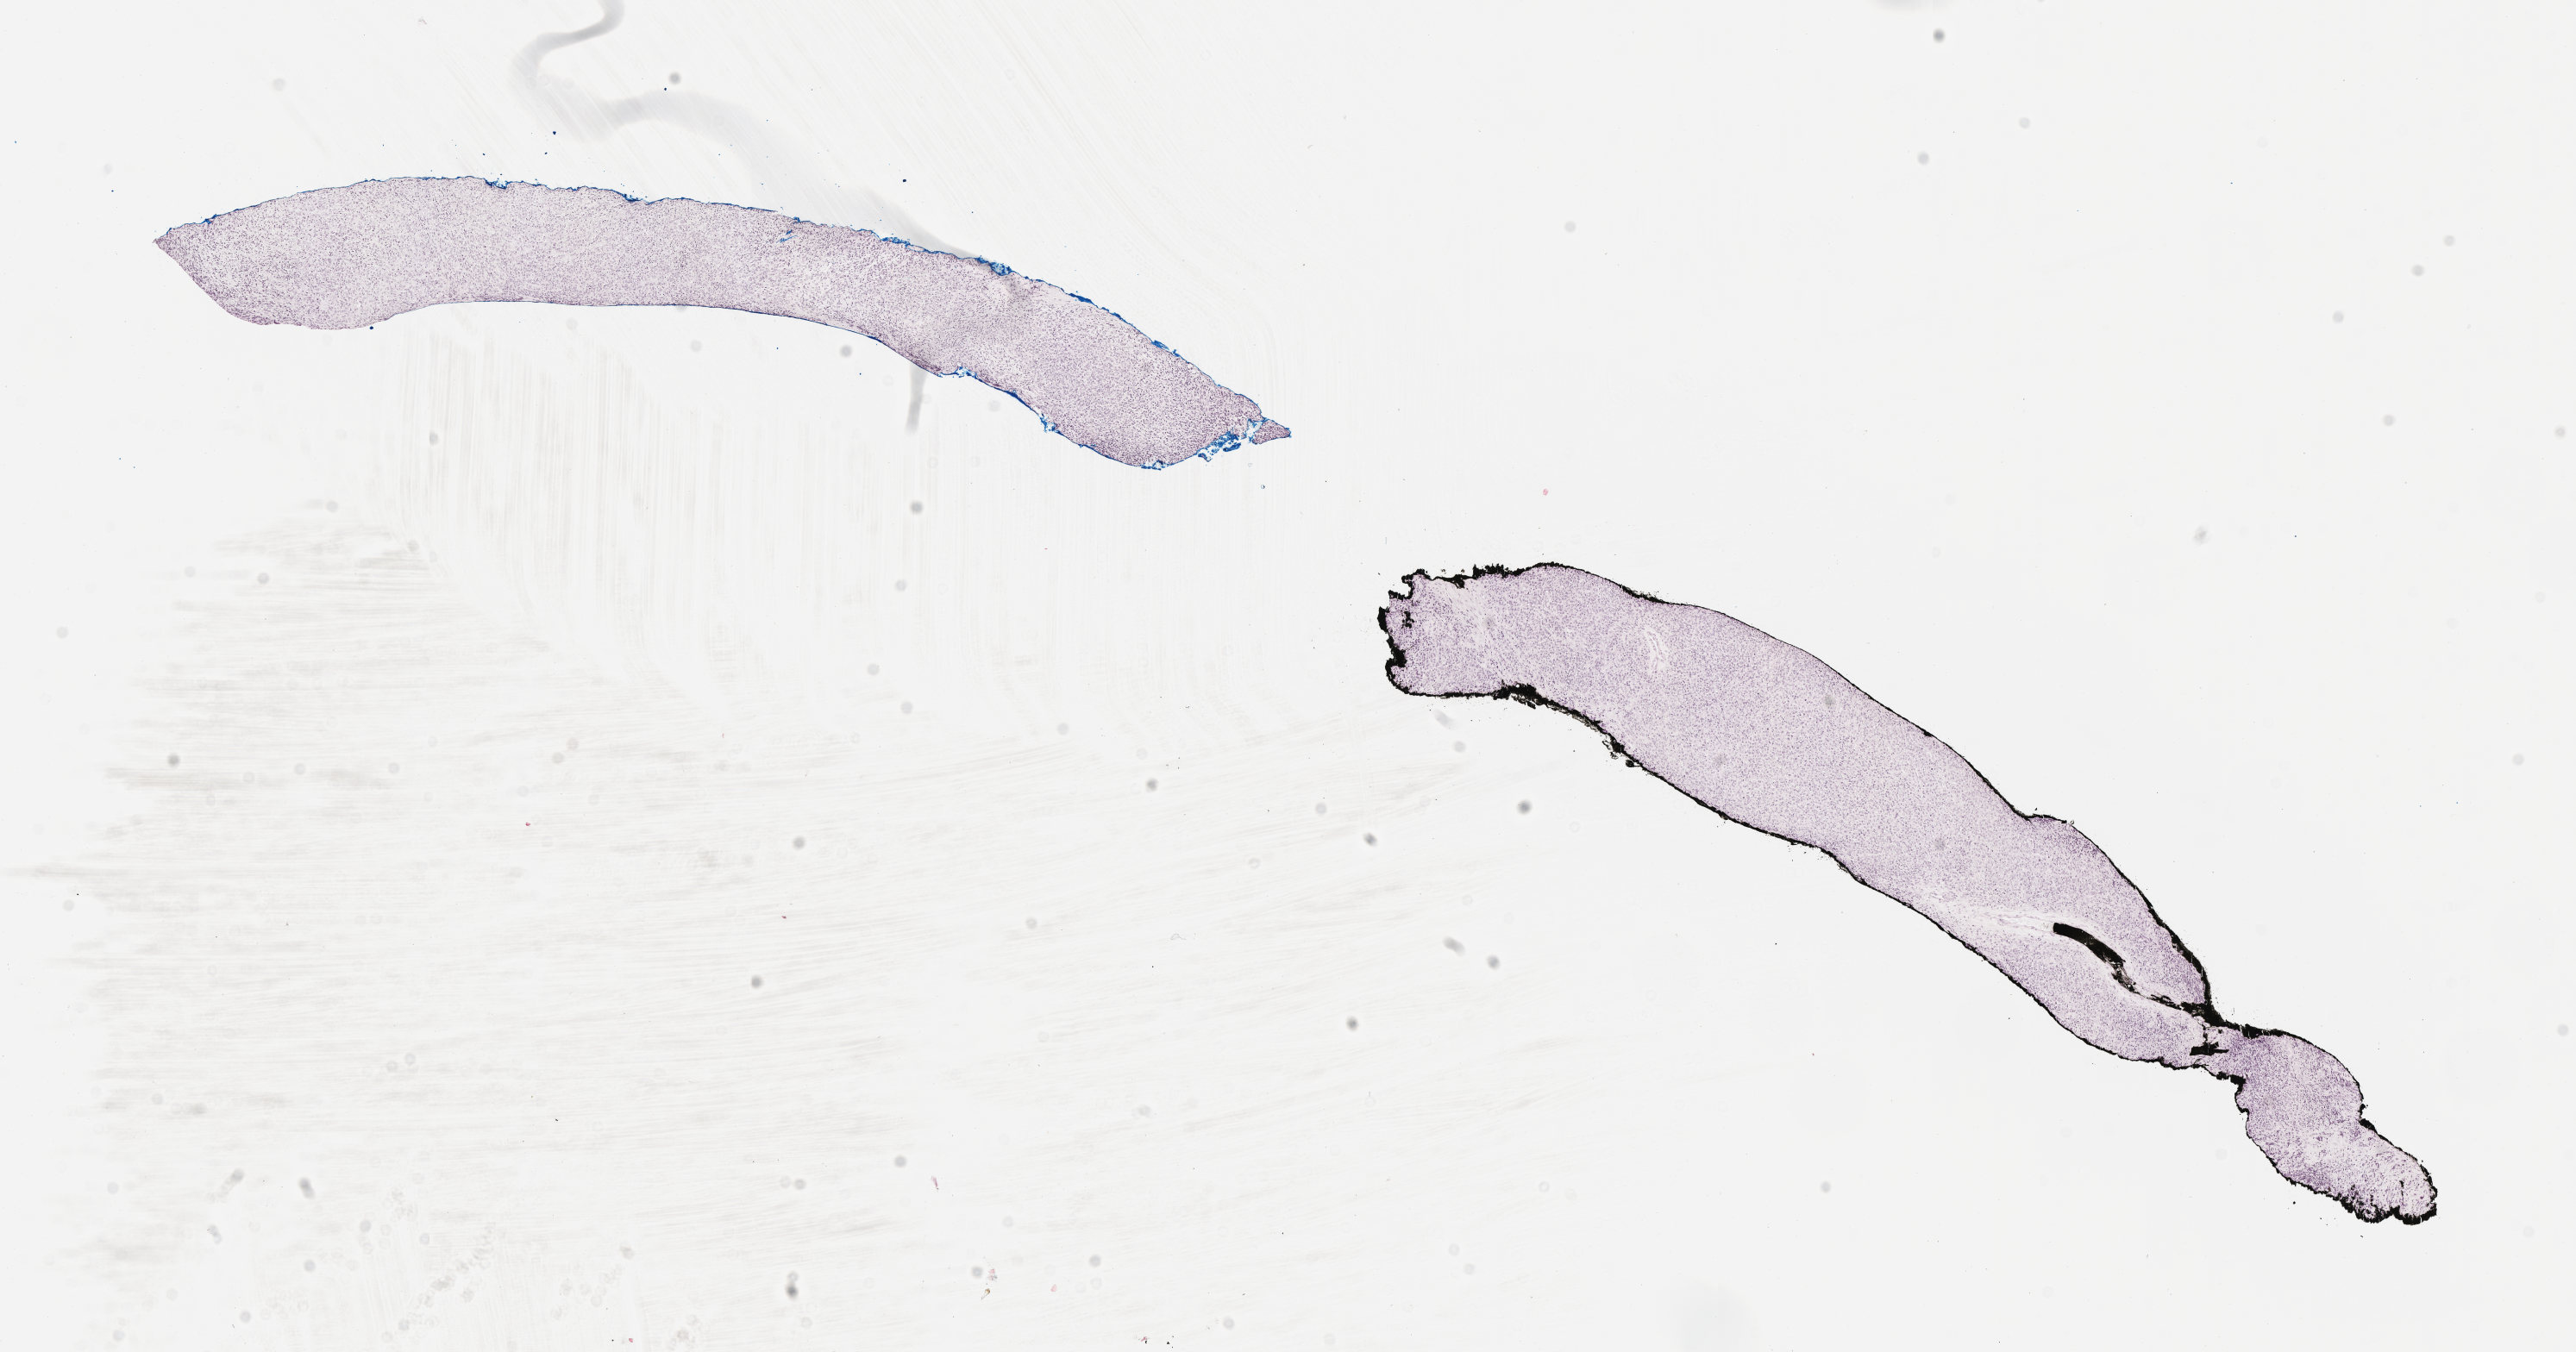
Whole-slide image, haematoxylin and eosin stain of tumor tissue — low-resolution overview of the scanned area, about 12.1 x 6.3 mm, FFPE section, sample anatomic site: soft tissue, pelvis. Male patient, age at diagnosis 1.1 years.
Diagnosis: rhabdomyosarcoma; histological classification: embryonal rhabdomyosarcoma.